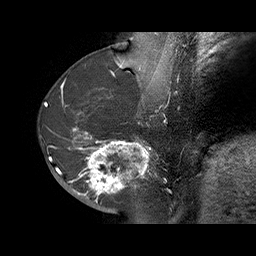
Breast MRI (dynamic contrast-enhanced), one sagittal slice. Slice 27 of 70 in the series (ordered by position). Dynamic contrast-enhanced series, time point 2 of 6 at this slice position (early post-contrast). 1.5 T. TE 4.5 ms, TR 32.4 ms. 256 × 256 image matrix. Female patient. Case-level facts recorded for this patient, not image findings: setting: breast cancer imaged before/during neoadjuvant chemotherapy; receptor status: HR-positive, HER2-negative.
Annotated regions visible in this slice (semi-automatic segmentation, software-assisted and operator-edited):
- analysis volume of interest (the breast-tissue region the enhancement analysis was run in; not a lesion): bounding box <71,128,159,202> (left, top, right, bottom; pixels)
- tumour enhancement mask (voxels above the 100 % enhancement threshold inside the analysis volume of interest): <71,128,150,201>